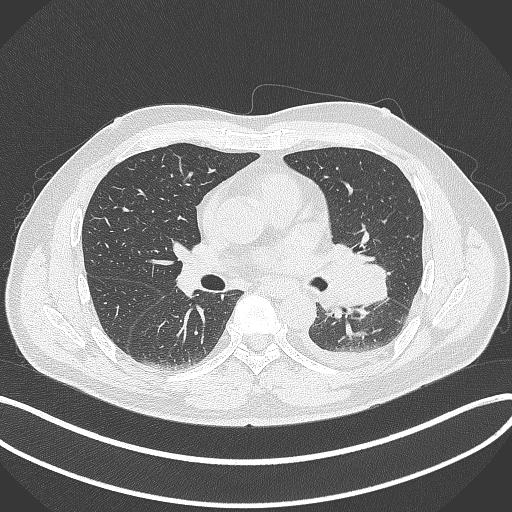
Chest CT, one axial slice. Position 192 of 342 along the scan axis. 120 kVp. Lung window (W 1500 / L -600 HU). 512 × 512 image matrix. Male patient, age 58 years. From the clinical record (not read from this slice): clinical TNM (as recorded): T3 N1 M1b.
Structures marked on this image (rectangle marked by the reading radiologist):
- lung tumour (recorded histology: small cell carcinoma): bounding box <324,239,386,317> (left, top, right, bottom; pixels)